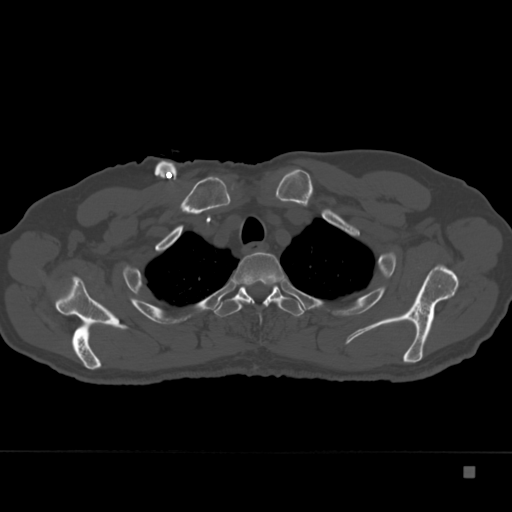
CT including the spine, one axial slice; slice 293 of 332 in the series (ordered by position); reconstruction kernel Br40s; bone window (W 1800 / L 400 HU); 1.5 mm slice thickness; 512 × 512 image matrix, field of view 389 × 389 mm. Male patient, age 72 years. Case-level facts recorded for this patient, not image findings: primary cancer: skeletal.
Outlined on this slice (semi-automatic segmentation, software-assisted and operator-edited):
- T2 vertebra: bounding box <232,251,285,307> (left, top, right, bottom; pixels)
- T3 vertebra: <214,283,304,317>